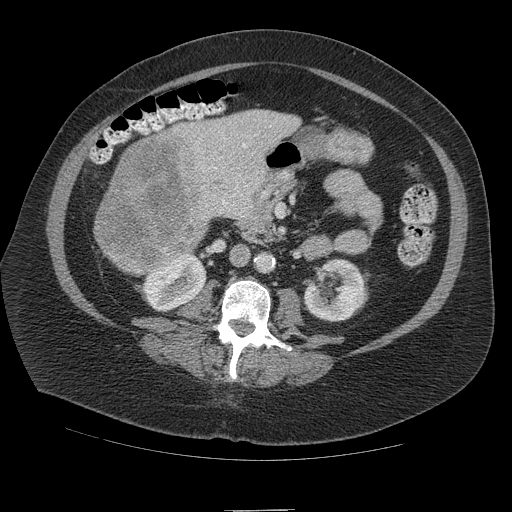
Contrast-enhanced abdominal CT (liver protocol), one axial slice. Position 36 of 109 along the scan axis. Reconstruction kernel STANDARD. Soft-tissue window (W 400 / L 40 HU). 512 × 512 image matrix, field of view 420 × 420 mm. Case-level facts recorded for this patient, not image findings: diagnosis: hepatocellular carcinoma (patient treated with transarterial chemoembolisation; whether this scan precedes or follows treatment is not stated here); TNM stage (as recorded): Stage-IVB; Child-Pugh class: A; tumour differentiation: poorly differentiated; tumour nodularity: multinodular.
Outlined on this slice (semi-automatically segmented with operator editing):
- liver parenchyma outside the tumour (the mass and vessels are separate outlines, so this box may not span the whole liver): bounding box [x1, y1, x2, y2] px = [94, 110, 300, 274]
- mass: [95, 130, 207, 273]
- liver vessels: [221, 137, 248, 205]